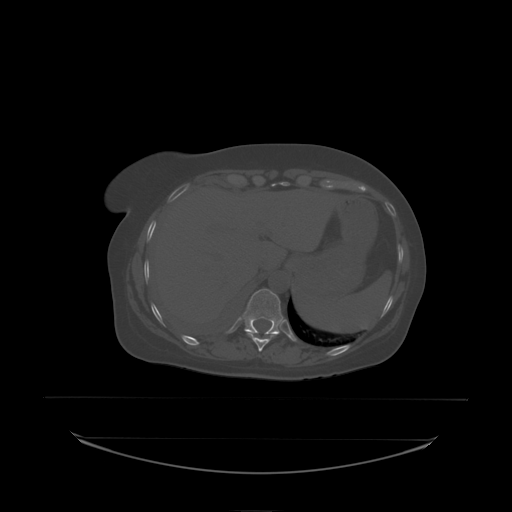
CT including the spine, one axial slice; slice 108 of 242 in the series (ordered by position); bone window (W 1800 / L 400 HU); 2.5 mm slice thickness; 512 × 512 image matrix. Female patient, age 53 years. From the clinical record (not read from this slice): primary cancer: lung; vertebrae with lytic lesions (as recorded): T7, L1.
Structures marked on this image (semi-automatically segmented with operator editing):
- T10 vertebra: bounding box (x1, y1, x2, y2) in pixels: (247, 334, 255, 338)
- T11 vertebra: (243, 289, 284, 335)